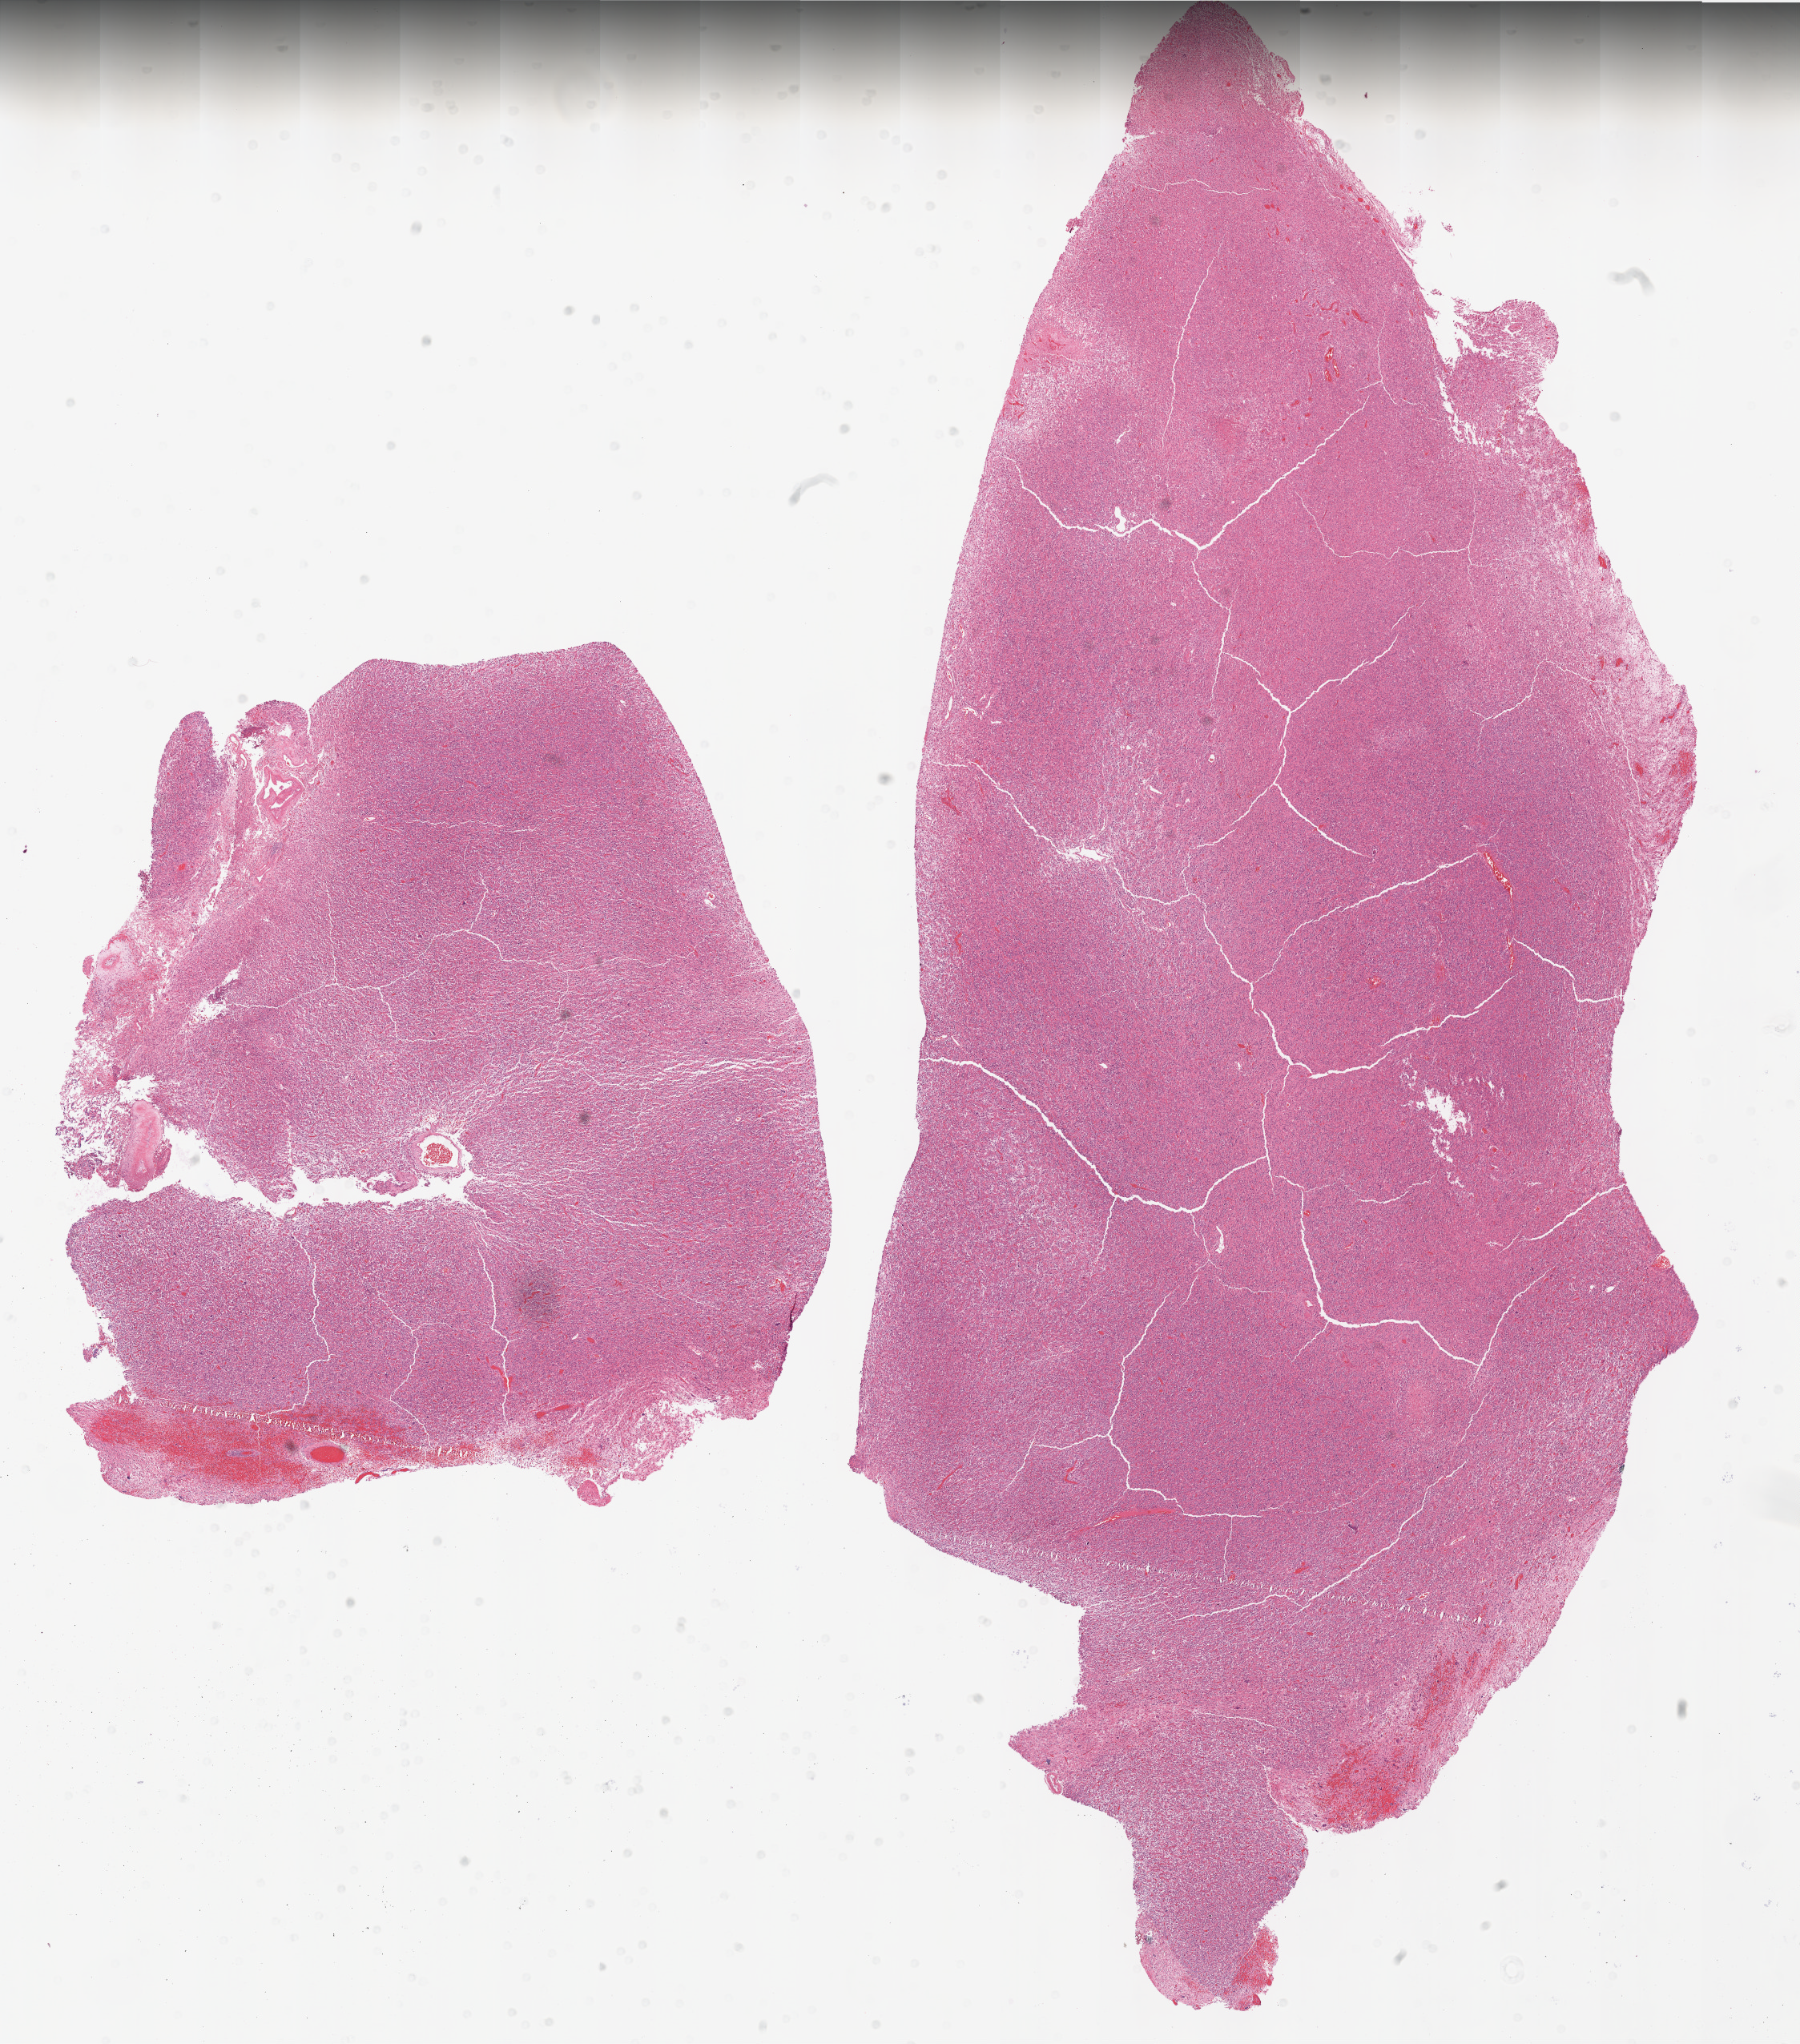
Whole-slide histology image, H&E — a low-resolution overview of the entire scanned area, about 18.0 x 20.4 mm (acquisition: 20x scan); formalin-fixed paraffin-embedded (FFPE) diagnostic section; primary tumour sample from the brain. Patient: male, age at initial diagnosis 68 years.
Diagnosis: Glioblastoma.